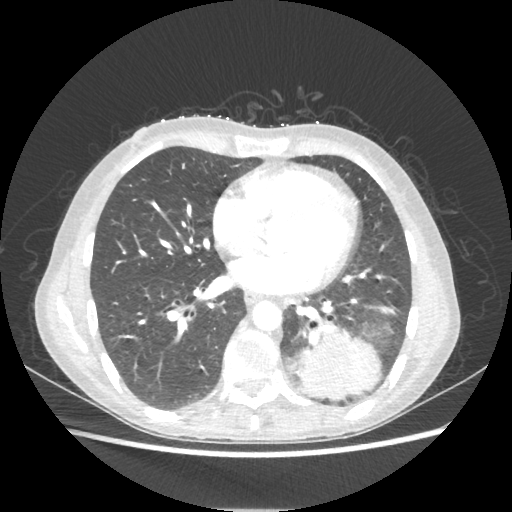
Chest CT, one axial slice; position 92 of 221 along the scan axis; reconstruction kernel STANDARD; 80 kVp; lung window (W 1500 / L -600 HU); 1.25 mm slice thickness; 512 × 512 image matrix. Female patient, age 53 years. Case-level facts recorded for this patient, not image findings: clinical TNM (as recorded): T3 N0 M0.
Structures marked on this image (rectangle marked by the reading radiologist):
- lung tumour (recorded histology: adenocarcinoma): box from (x=294, y=328) to (x=380, y=400) px